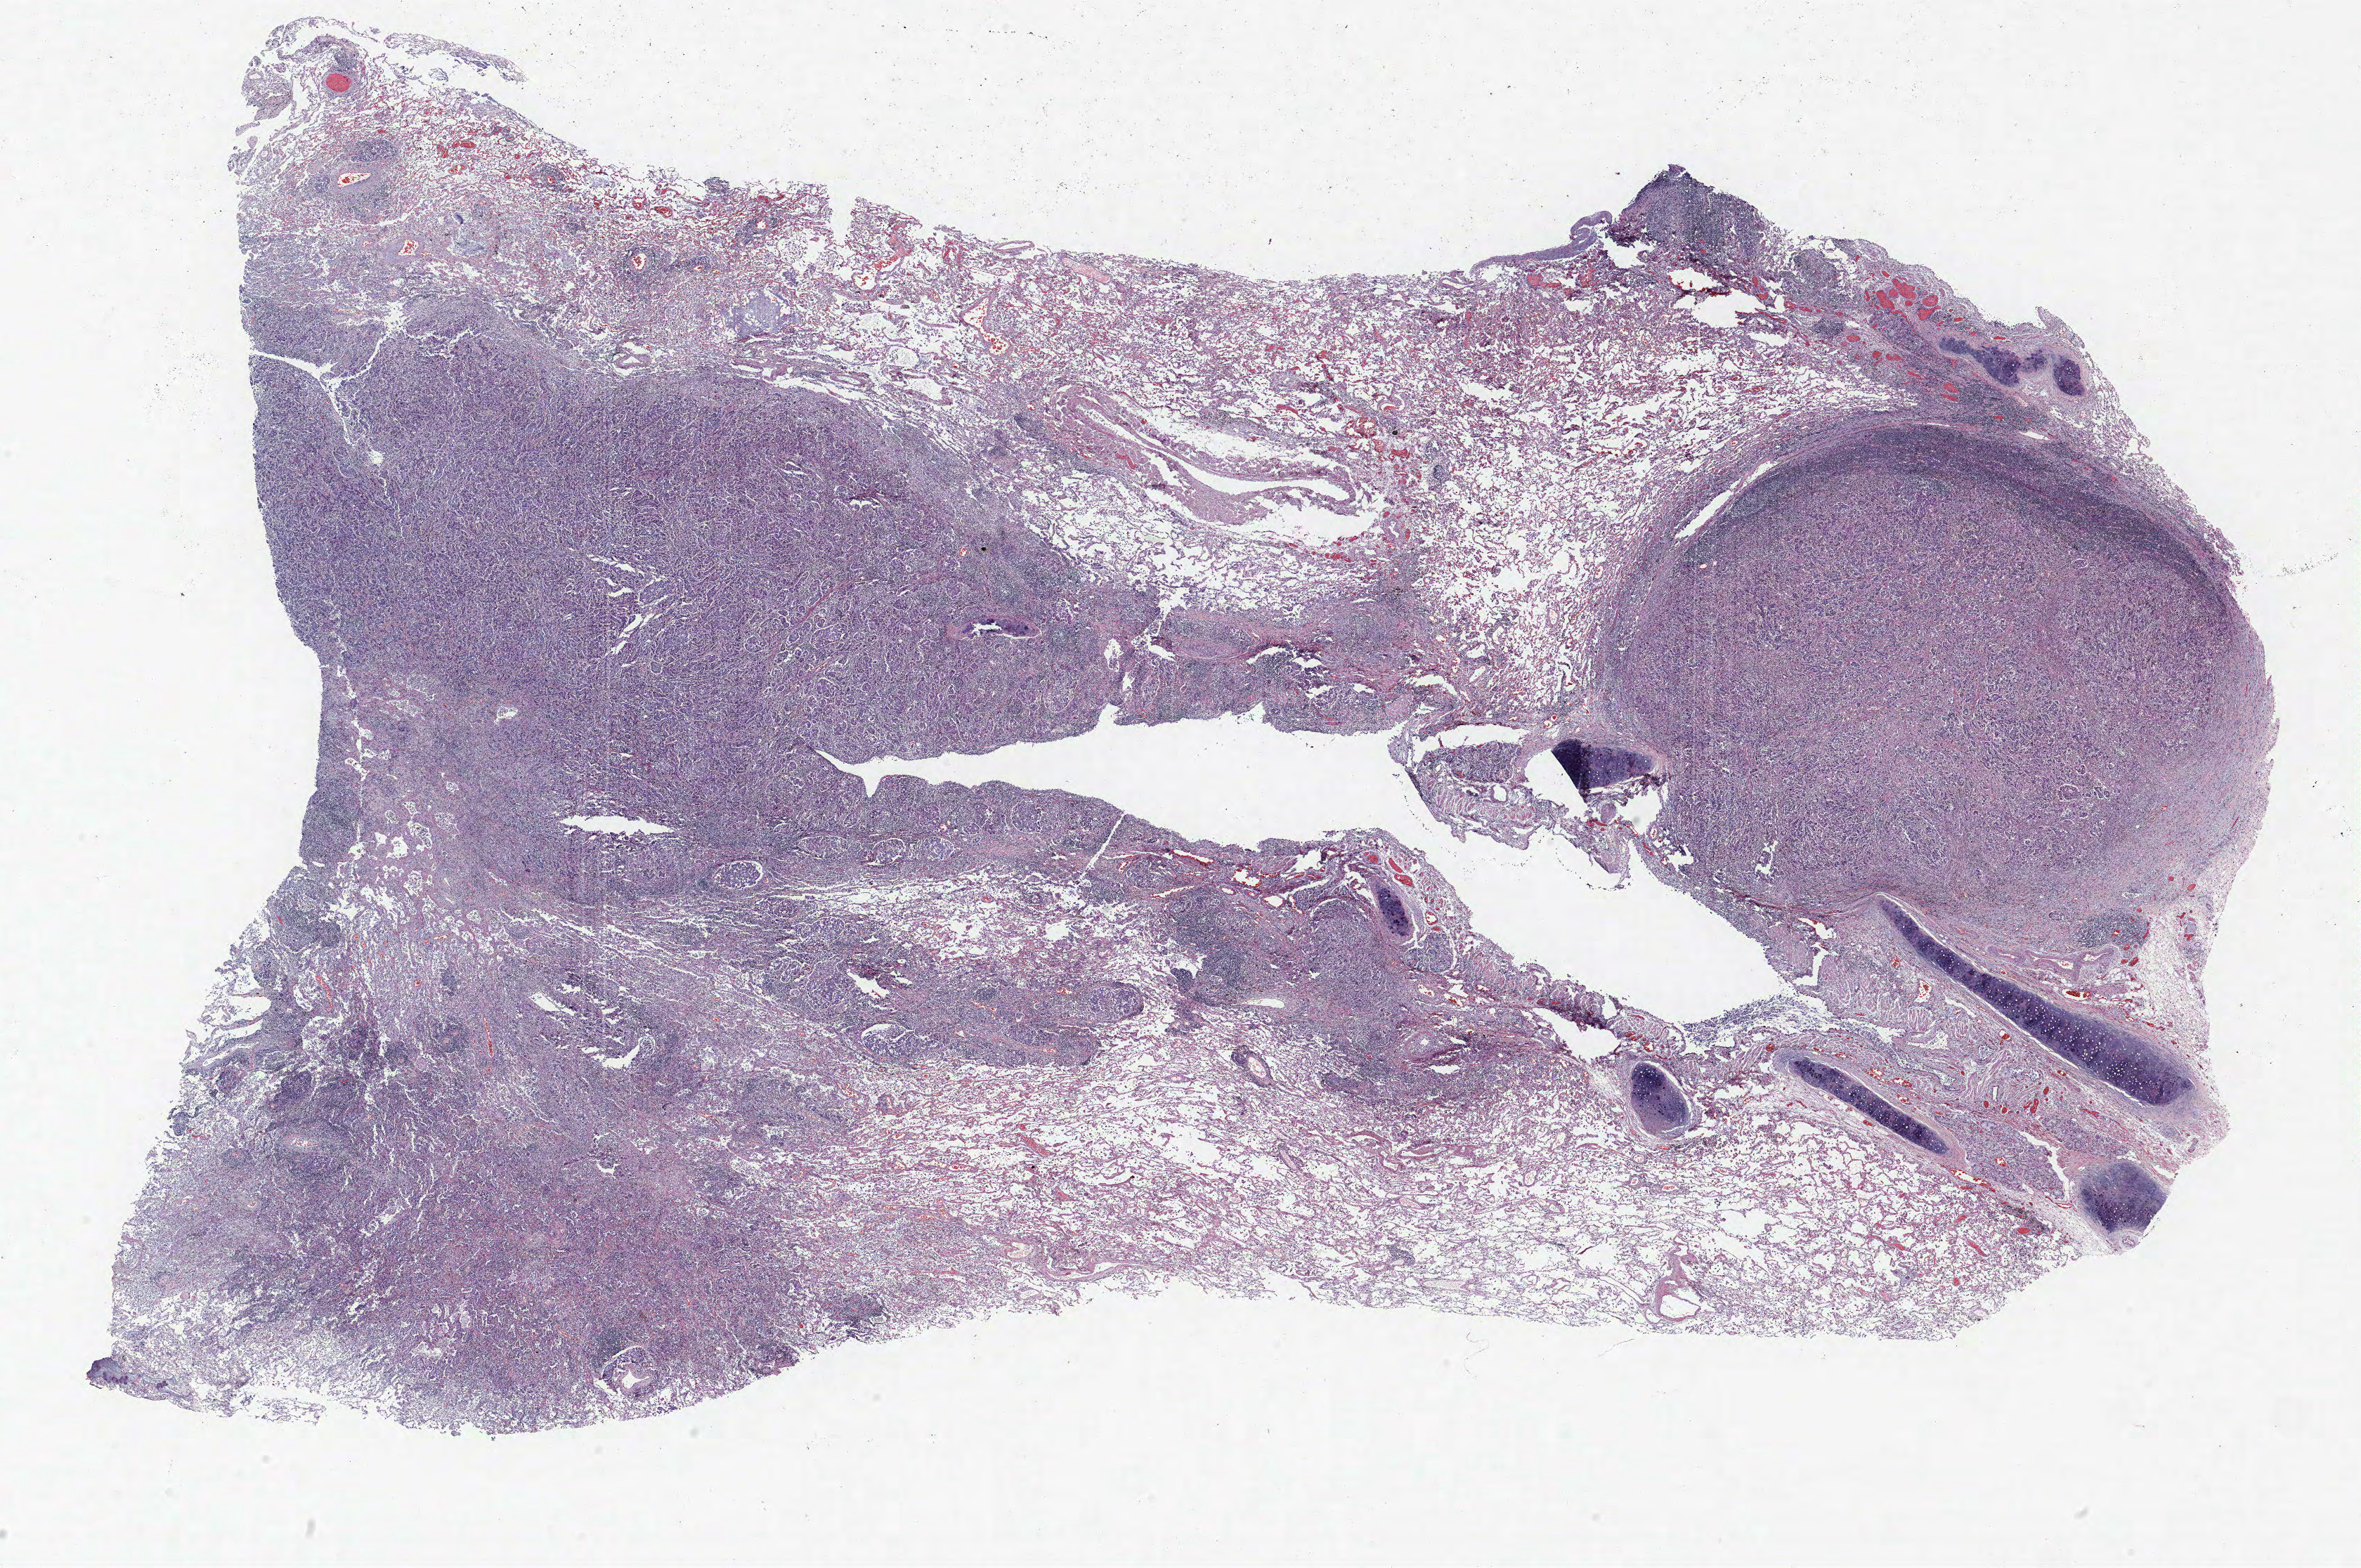
Hematoxylin and eosin (H&E) stained whole-slide image — shown as a low-resolution overview of the whole scanned area (about 26.9 x 17.9 mm); FFPE section; lung. Male, age 65 at enrolment. Current smoker at enrolment. Grade: poorly differentiated (G3).
- primary tumour location (clinical record): left upper lobe
- stage (AJCC 6th edition): IIIA
- participant's lung-cancer diagnosis: Carcinoma, NOS (ICD-O-3 8010/3)
- tumour size (pathology): 25 mm